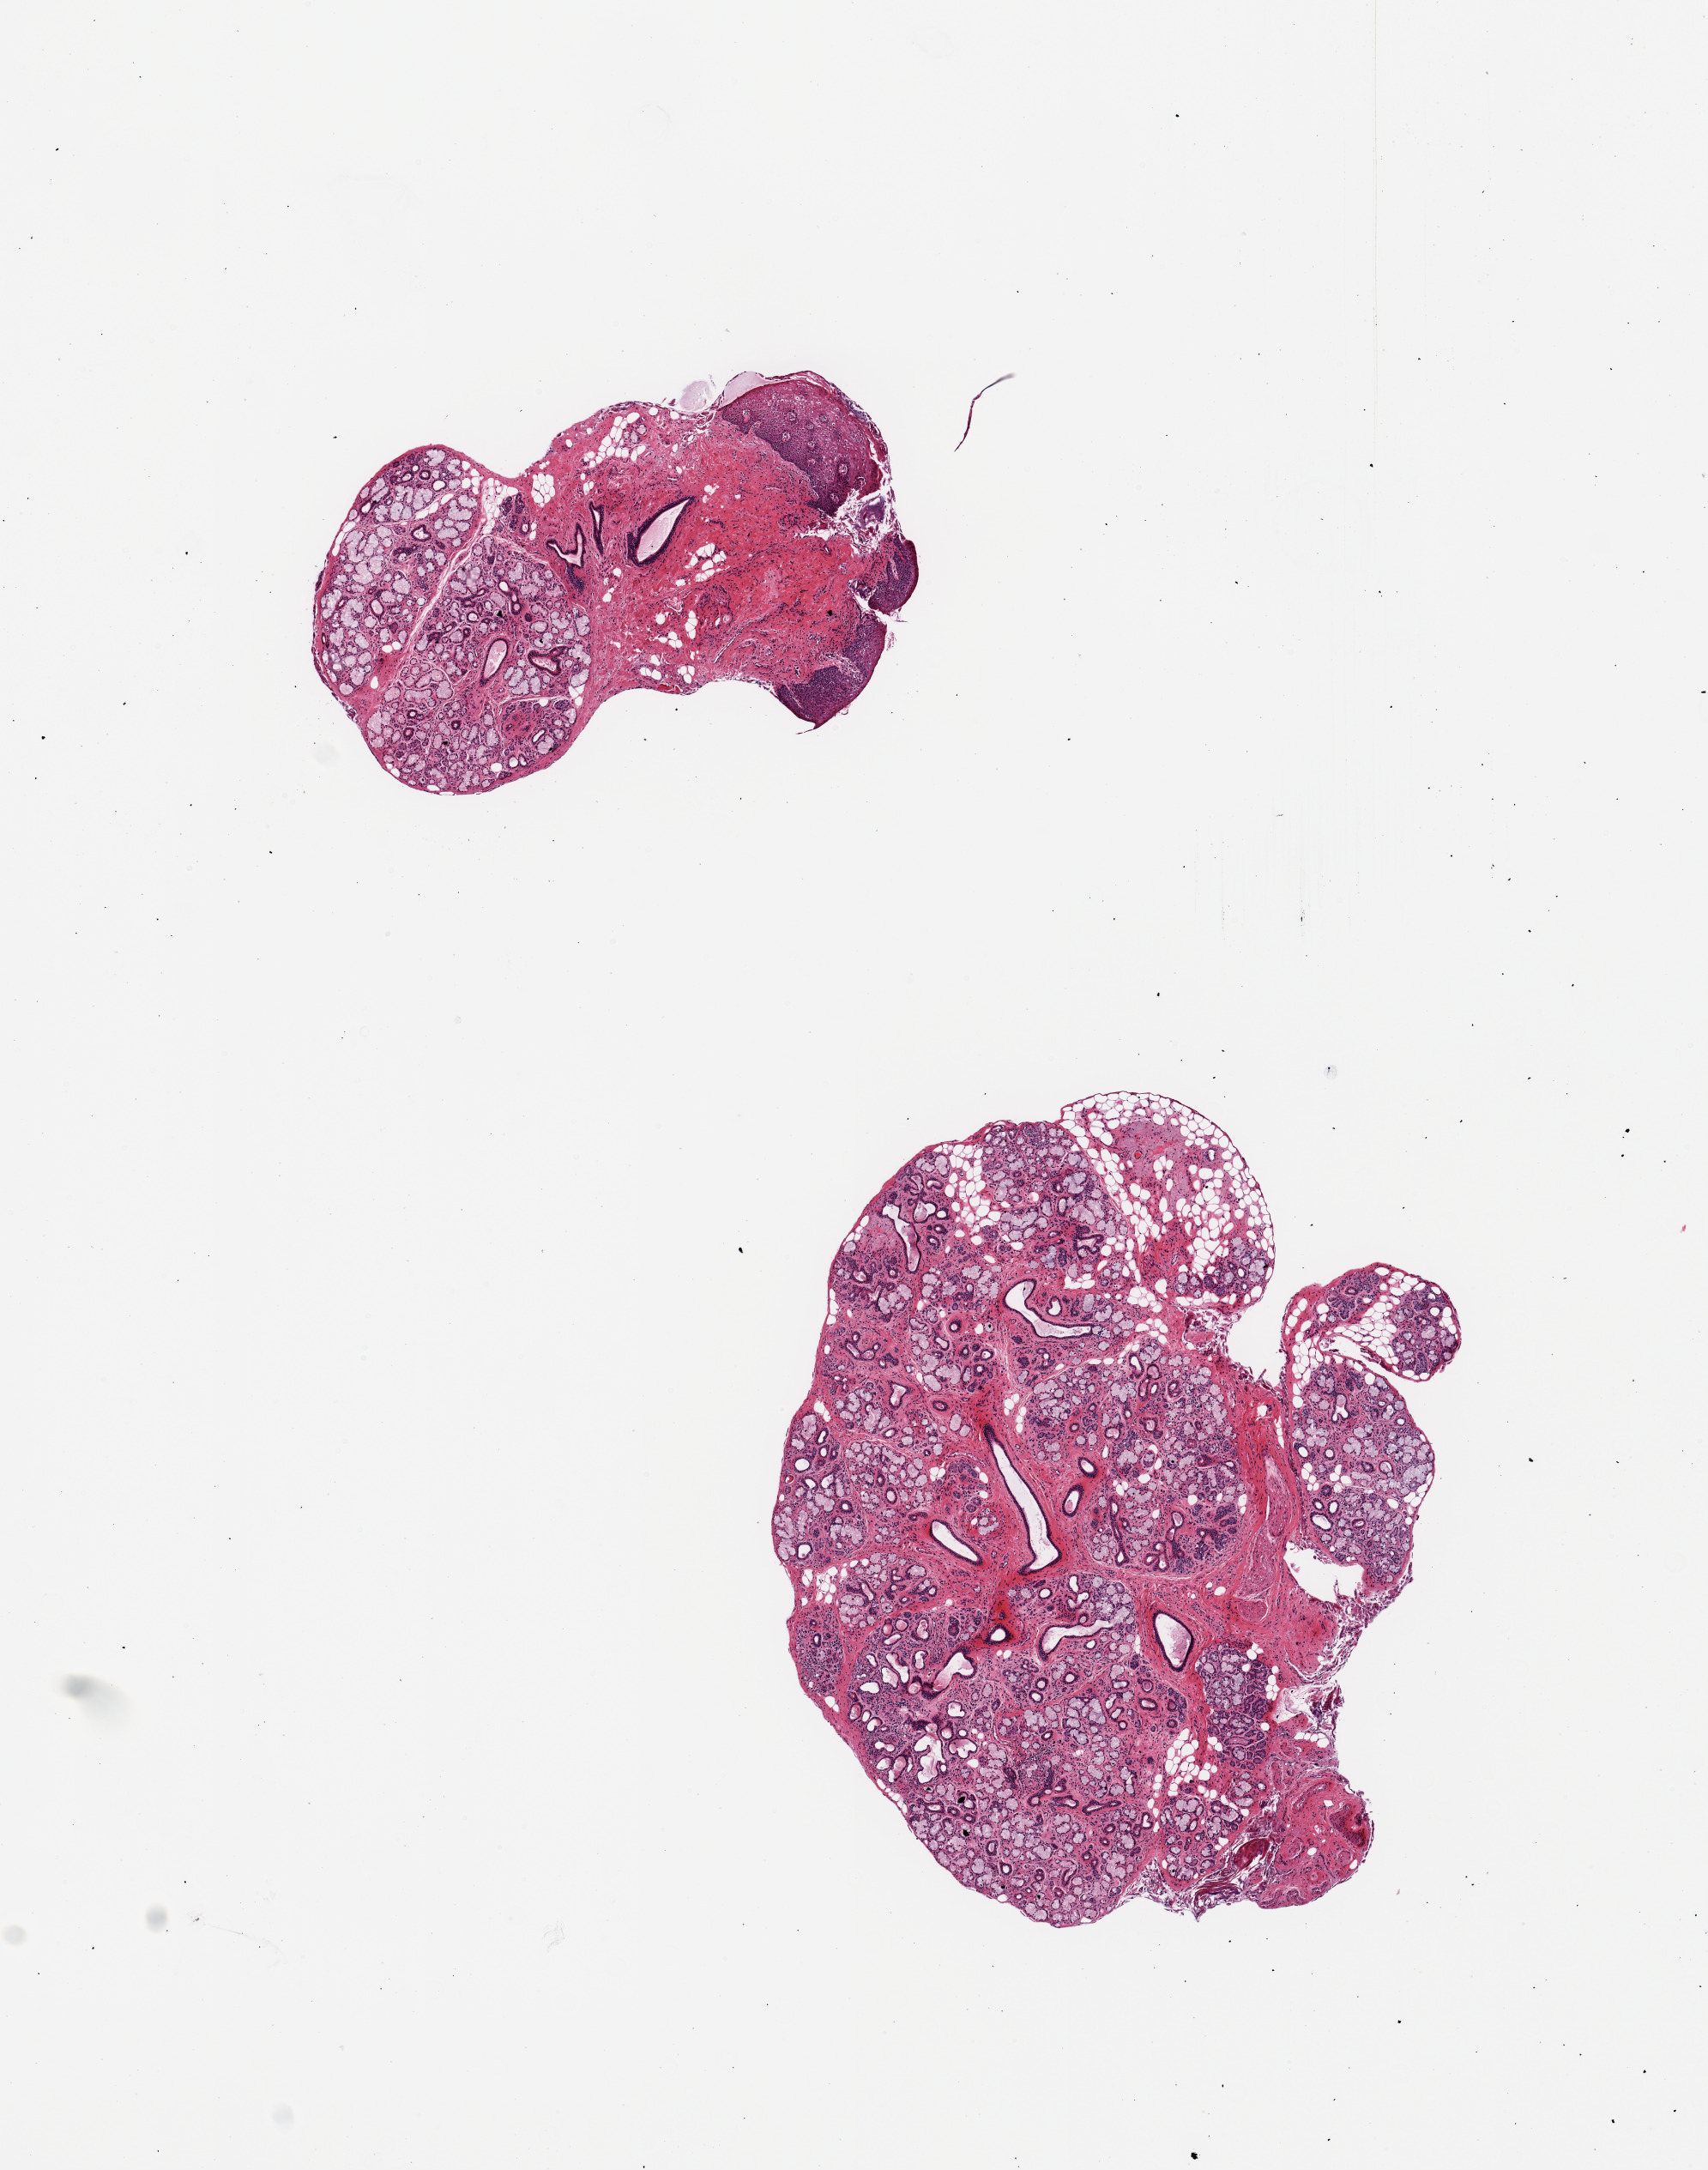
H&E whole-slide image, brightfield, whole scanned area (about 7.9 x 10.0 mm) shown as a low-resolution overview, PAXgene-fixed, paraffin-embedded tissue, sampled site (target tissue): minor salivary gland, donor tissue sample. Male donor.
Pathologist's review note for this sample: 2 pieces; larger is a well dissected gland; smaller contains gland with 50% skin and stroma.